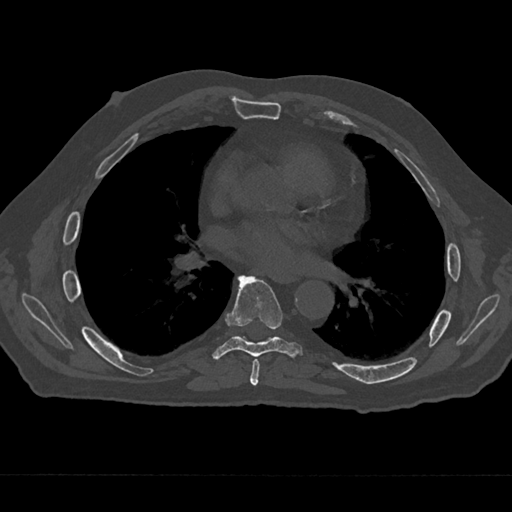
CT including the spine, one axial slice. Slice 372 of 797 in the series (ordered by position). Reconstruction kernel Br40s/3. Bone window (W 1800 / L 400 HU). 0.5 mm slice thickness. 512 × 512 image matrix. Male patient, age 75 years. From the clinical record (not read from this slice): primary cancer: renal.
Outlined on this slice (semi-automatic segmentation, software-assisted and operator-edited):
- T6 vertebra: bounding box (x1, y1, x2, y2) in pixels: (250, 359, 260, 386)
- T7 vertebra: (212, 276, 303, 360)